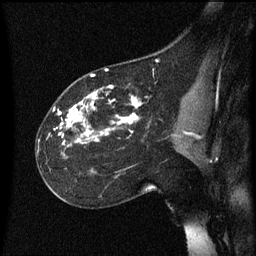
Breast MRI (dynamic contrast-enhanced), one sagittal slice; dynamic contrast-enhanced series, image 2 of 3 at this slice position (ordered by acquisition); 1.5 T; TE 4.2 ms, TR 8.4 ms; 256 × 256 image matrix, field of view 200 × 200 mm. Female patient, age 35 years. From the clinical record (not read from this slice): setting: breast cancer imaged before/during neoadjuvant chemotherapy; receptor status: HER2-positive.
Structures marked on this image (semi-automatically segmented with operator editing):
- analysis volume of interest (the breast-tissue region the enhancement analysis was run in; not a lesion): bounding box (x1, y1, x2, y2) in pixels: (36, 72, 178, 173)
- tumour enhancement mask (voxels above the 70 % enhancement threshold inside the analysis volume of interest): (56, 74, 142, 145)